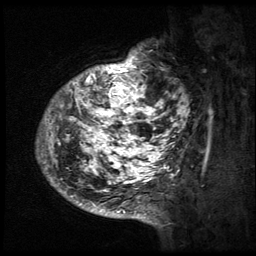
Breast MRI (dynamic contrast-enhanced), one sagittal slice. Slice 14 of 64 in the series (ordered by position). 3 images stored at this slice position (order not interpretable as contrast timing). 1.5 T. TE 4.2 ms, TR 9 ms. 2.5 mm slice thickness. 256 × 256 image matrix, field of view 180 × 180 mm. Female patient, age 50 years. Case-level facts recorded for this patient, not image findings: setting: breast cancer imaged before/during neoadjuvant chemotherapy; receptor status: triple-negative.
Outlined on this slice (semi-automatic segmentation, software-assisted and operator-edited):
- analysis volume of interest (the breast-tissue region the enhancement analysis was run in; not a lesion): box from (x=36, y=39) to (x=194, y=212) px
- tumour enhancement mask (voxels above the 140 % enhancement threshold inside the analysis volume of interest): (x=37, y=48)–(x=191, y=212)